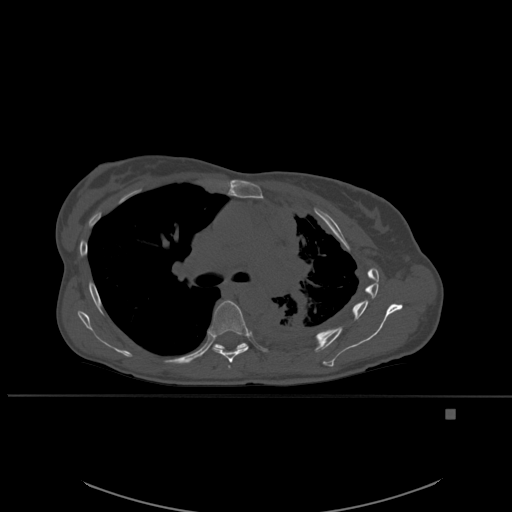
CT including the spine, one axial slice. Bone window (W 1800 / L 400 HU). 1.5 mm slice thickness. 512 × 512 image matrix. Patient: female, 45 years. Case-level facts recorded for this patient, not image findings: primary cancer: lung.
Annotated regions visible in this slice (semi-automatically segmented with operator editing):
- T5 vertebra: box from (x=228, y=365) to (x=230, y=369) px
- T6 vertebra: (x=209, y=300)–(x=249, y=363)
- T7 vertebra: (x=214, y=342)–(x=248, y=350)